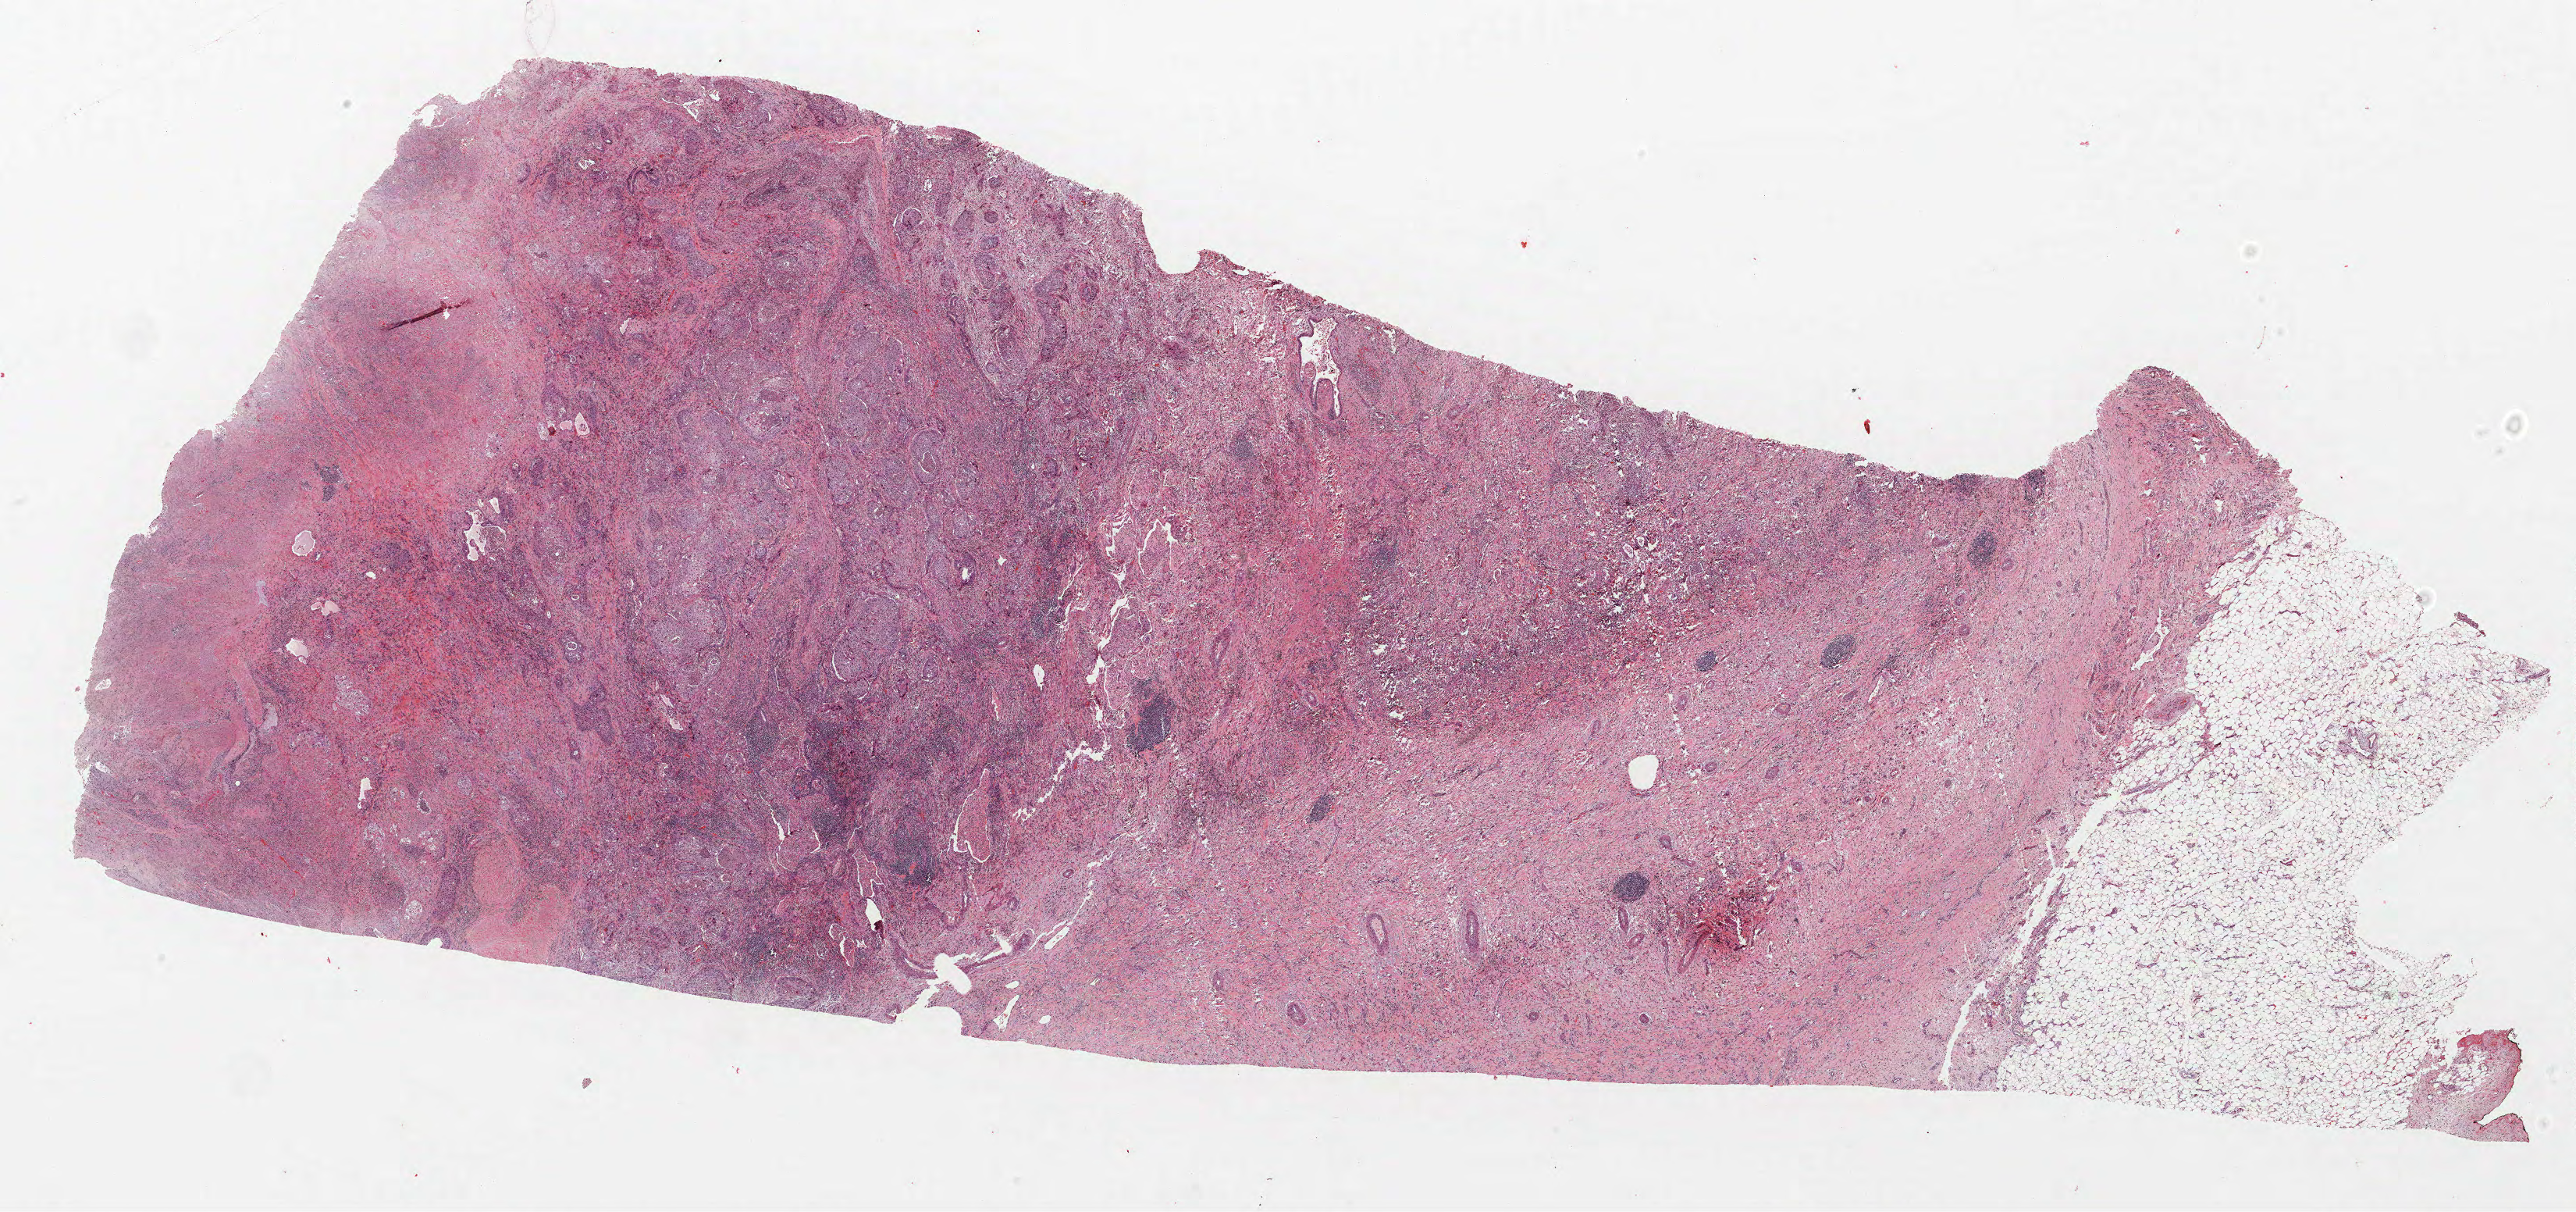
Whole-slide histology image, H&E — shown as a low-resolution overview of the whole scanned area (about 26.4 x 12.4 mm), formalin-fixed paraffin-embedded (FFPE) section, lung. Male, age 63 at enrolment. Grade: moderately differentiated (G2).
- participant's lung-cancer diagnosis: Squamous cell carcinoma, NOS
- primary tumour location (clinical record): right upper lobe
- tumour size (pathology): 80 mm
- stage (AJCC 6th edition): IB